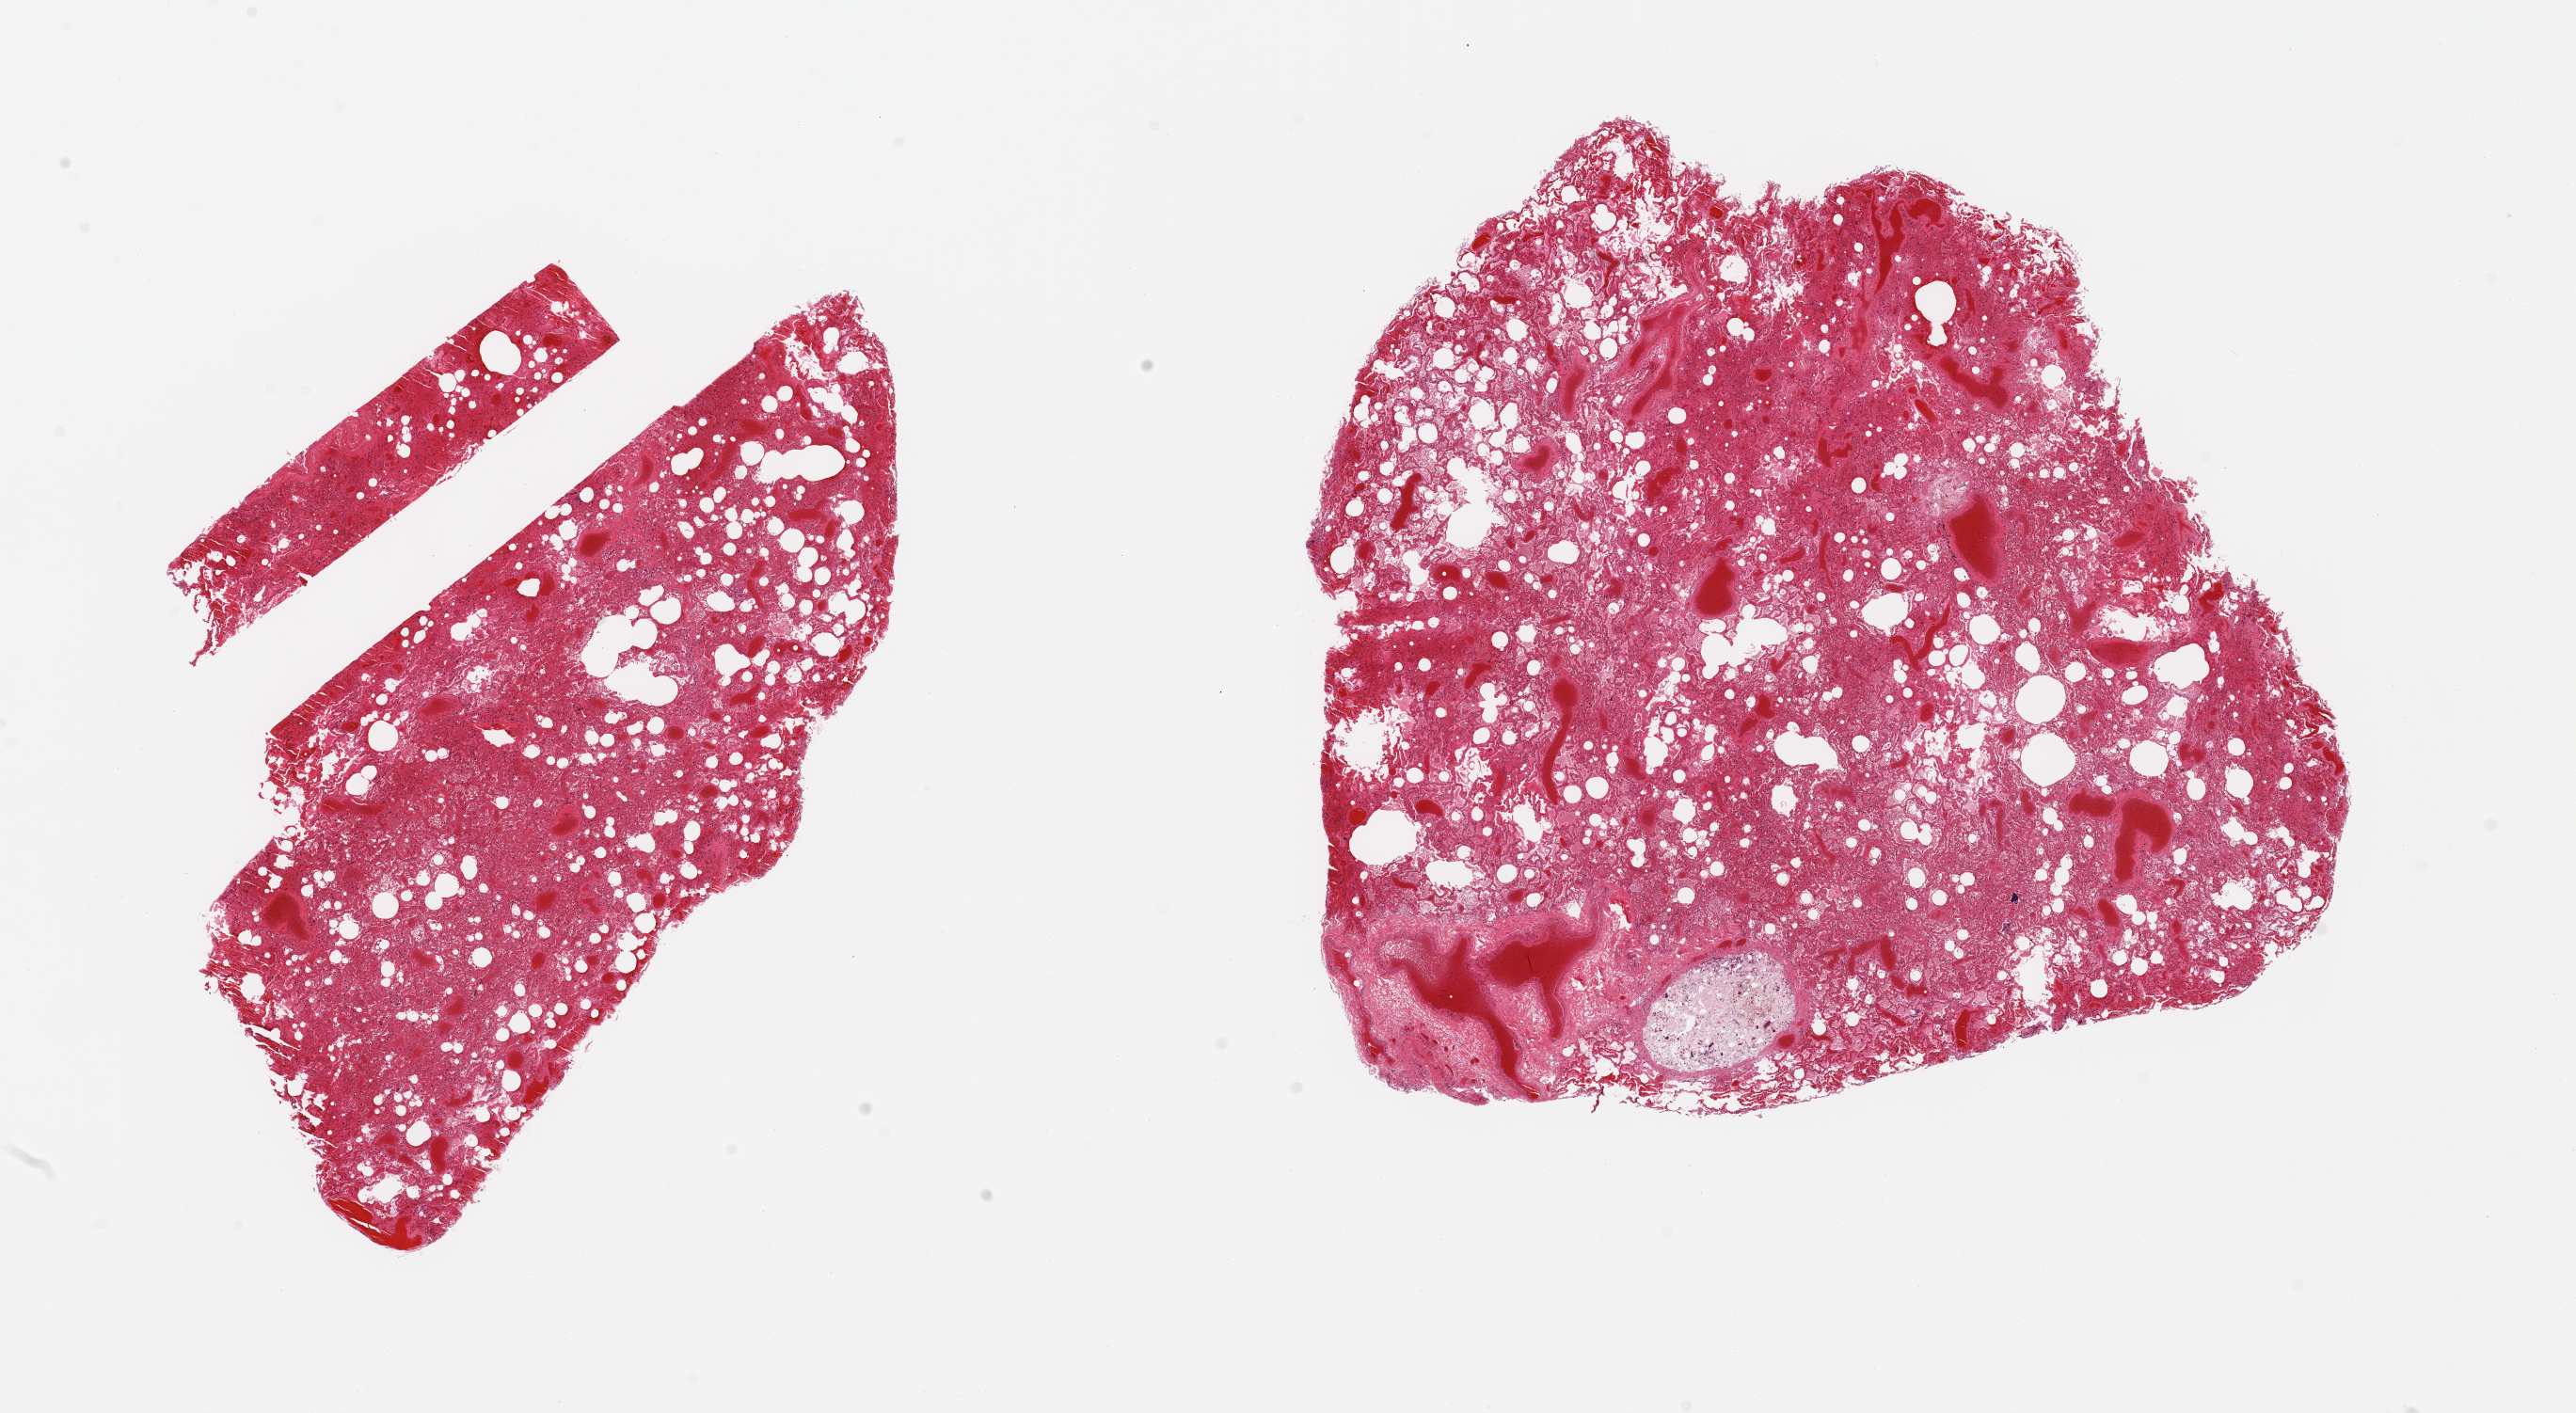
H&E whole-slide image, brightfield — whole scanned area (about 21.7 x 11.9 mm, acquisition: 20x scan) shown as a low-resolution overview, PAXgene-fixed paraffin-embedded (PFPE) section, sampled site (target tissue): lung, tissue donor sample. Donor sex: male.
Review note (as recorded): 2 pieces; marked congestion & alveolar hemorrhage; aspiration of foreign material in bronchus.